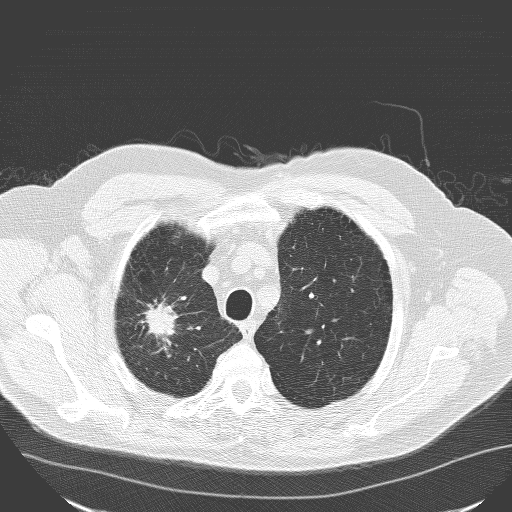
Chest CT (low-dose screening protocol), one axial image. Baseline screening round. Lung window (W 1500 / L -600 HU). 3.2 mm slice thickness. Lung (sharp) reconstruction kernel (D). Slice 134 of 160 in the series. Male, age 71 years at enrolment. Current smoker at enrolment.
• Expert reader's lesion annotation, bounding box <116,280,190,356> (left, top, right, bottom; pixels).
• The exam's reader record, not a measurement of the box and not confirmed to be the same lesion: non-calcified nodule or mass ≥4 mm, right upper lobe, 30 × 25 mm, spiculated (stellate) margins, soft tissue attenuation.
• Official screen result: positive, change unspecified: nodule(s) >= 4 mm or enlarging nodule(s), mass(es), or other non-specific abnormalities suspicious for lung cancer.
• Lung cancer was diagnosed 182 days after this screen: squamous cell carcinoma, NOS, right upper lobe, poorly differentiated (G3), stage IA (AJCC 6th edition), 30 mm at pathology.